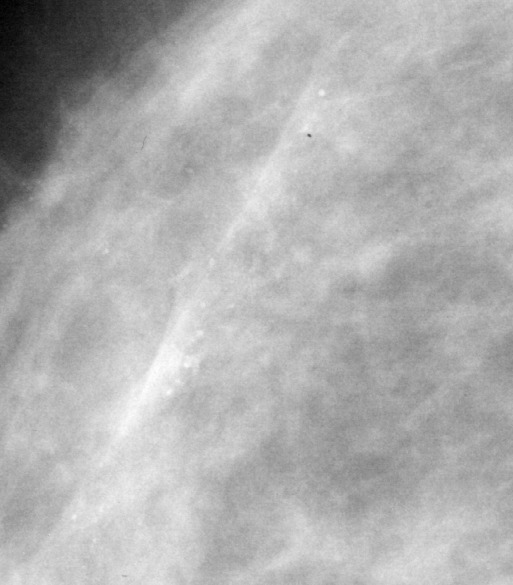
Cropped region of a digitized screen-film mammogram centred on a radiologist-marked abnormality; right breast; MLO view.
- Marked abnormality: calcifications, morphology pleomorphic, distribution segmental; BI-RADS assessment category 4; pathology (as recorded): benign.